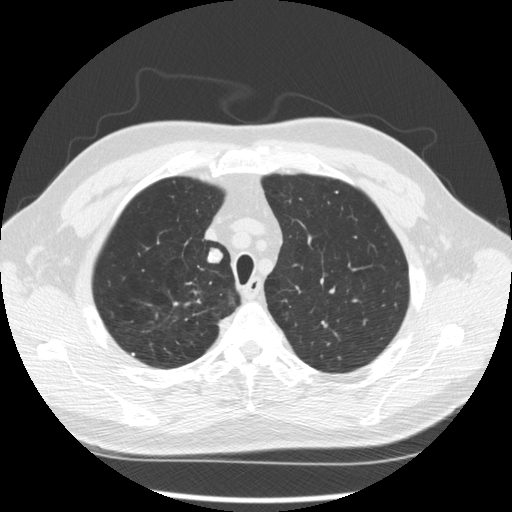
Axial slice from a low-dose chest CT screening exam. Second screening round (one year after baseline). Lung window (W 1500 / L -600 HU). Standard (soft-tissue) reconstruction kernel (STANDARD). Slice 52 of 289 in the series. Male, age 64 years at enrolment. Former smoker at enrolment.
• Lesion marked by an expert reader, bounding box [x1, y1, x2, y2] px = [192, 245, 226, 273].
• The screening reader recorded 3 non-calcified nodules or masses ≥4 mm on this exam (right upper lobe, right upper lobe, right upper lobe); which of them this box marks is not recorded.
• Official screen result: positive, other.